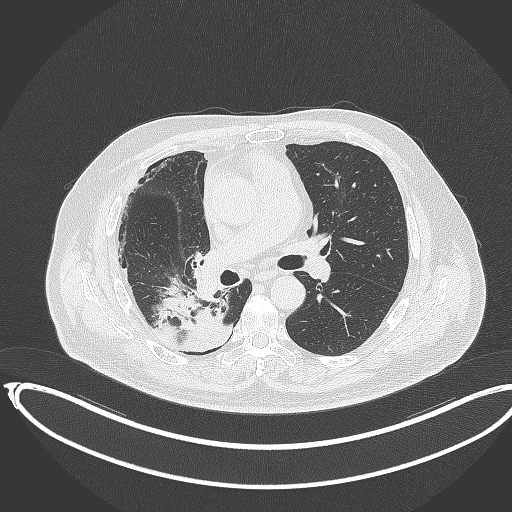
Chest CT, one axial slice; position 198 of 403 along the scan axis; reconstruction kernel B70f; 120 kVp; lung window (W 1500 / L -600 HU); 1 mm slice thickness; 512 × 512 image matrix, field of view 436 × 436 mm. Patient: male, 68 years. Case-level facts recorded for this patient, not image findings: clinical TNM (as recorded): T2a N0 M0.
Annotated regions visible in this slice (rectangle marked by the reading radiologist):
- lung tumour (recorded histology: adenocarcinoma): bounding box [x1, y1, x2, y2] px = [153, 292, 231, 356]